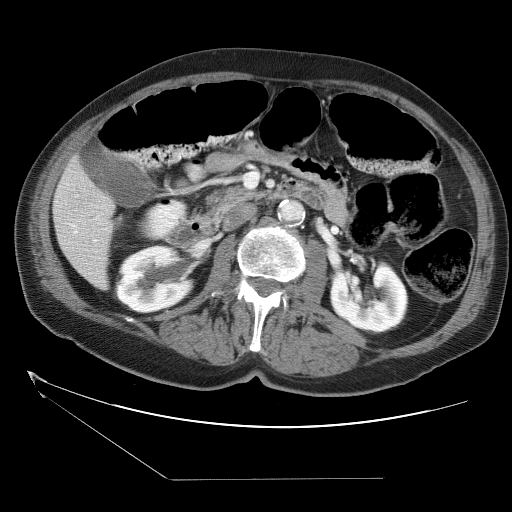
Contrast-enhanced abdominal CT (liver protocol), one axial slice; slice 9 of 38 in the series (ordered by position); 120 kVp; one of 2 acquisitions stored at this slice position; soft-tissue window (W 400 / L 40 HU); 5 mm slice thickness; 512 × 512 image matrix. From the clinical record (not read from this slice): diagnosis: hepatocellular carcinoma (patient treated with transarterial chemoembolisation; whether this scan precedes or follows treatment is not stated here); TNM stage (as recorded): Stage-II; Child-Pugh class: A; tumour differentiation: moderately differentiated.
Structures marked on this image (semi-automatically segmented with operator editing):
- liver parenchyma outside the tumour (the mass and vessels are separate outlines, so this box may not span the whole liver): bounding box [x1, y1, x2, y2] px = [52, 154, 114, 288]
- liver vessels: [68, 223, 98, 242]